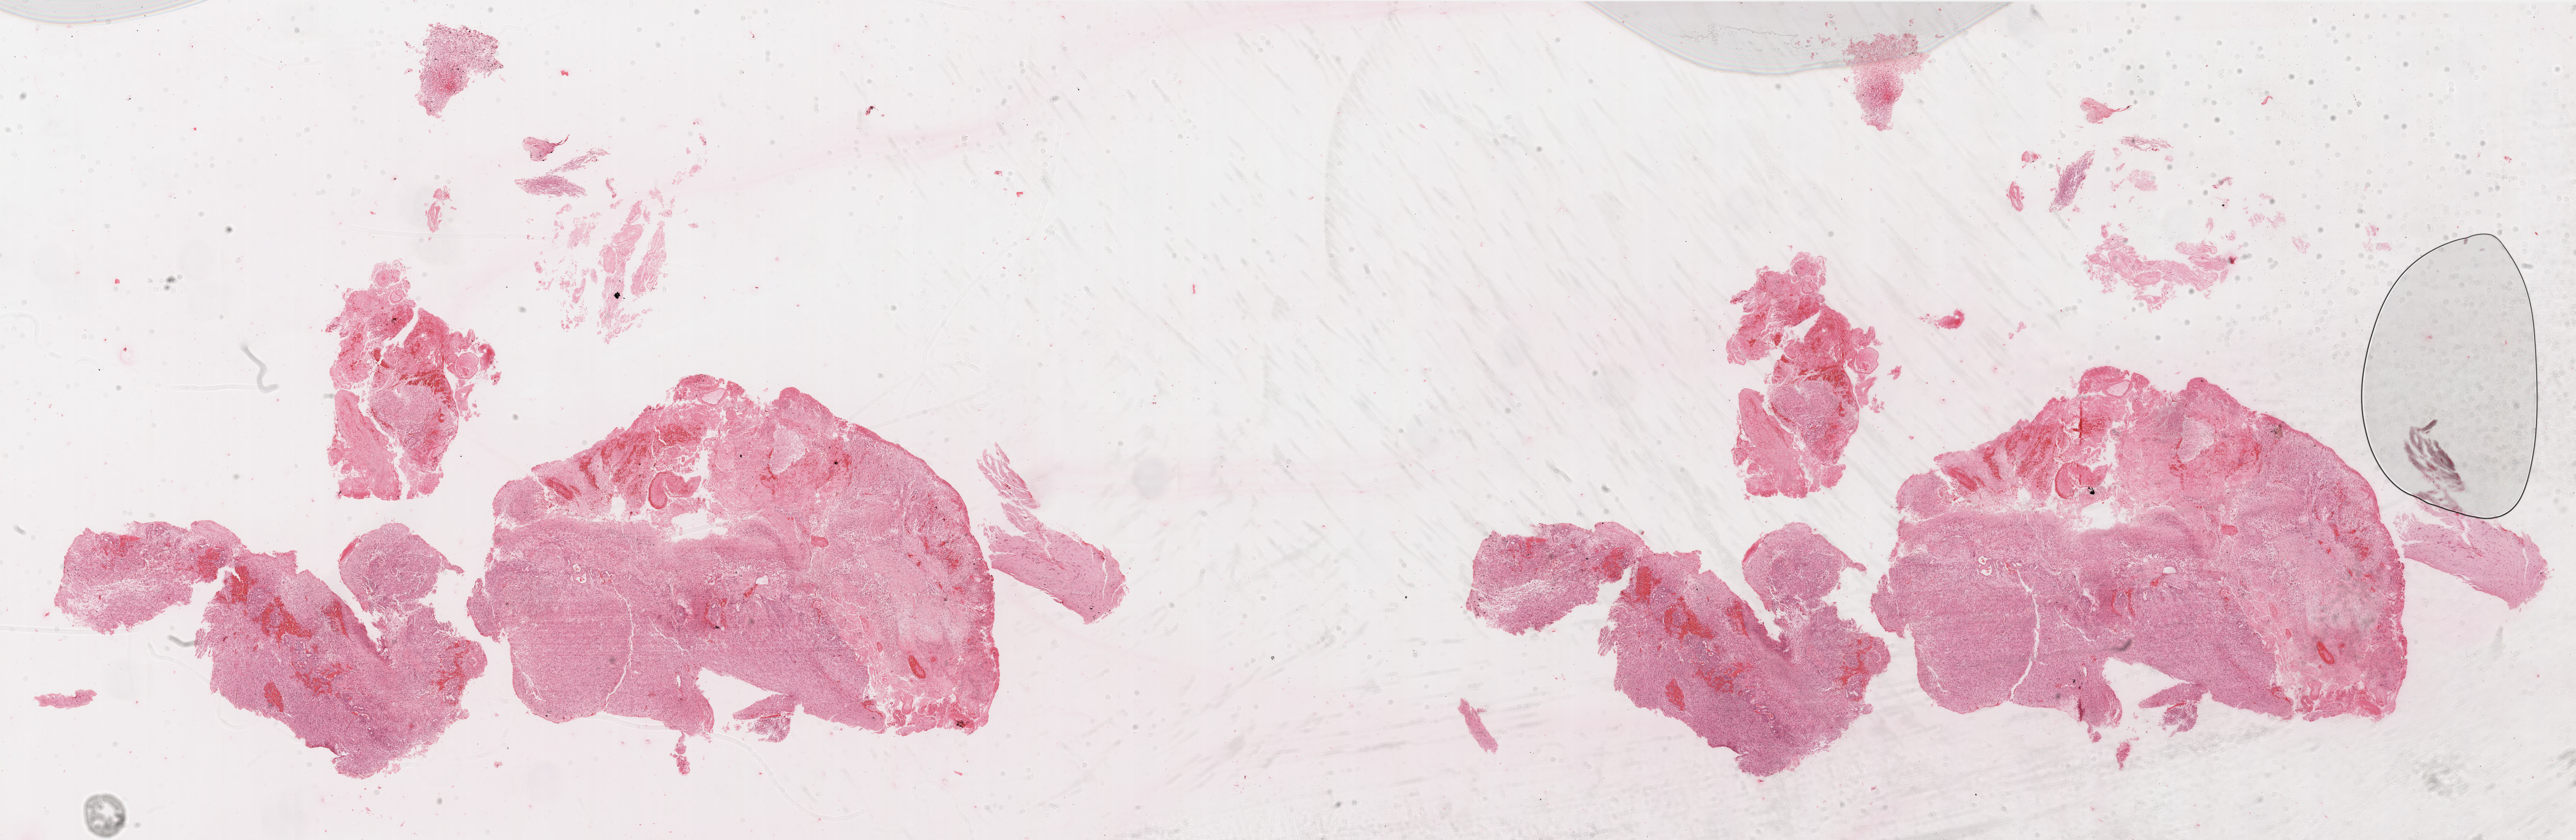
H&E whole-slide image — low-resolution overview of the scanned area, about 35.0 x 11.4 mm (slide scanned at 20x). FFPE section. Sample: primary tumour, brain. Patient: male, age at initial diagnosis 67 years.
Histologic diagnosis: Glioblastoma.